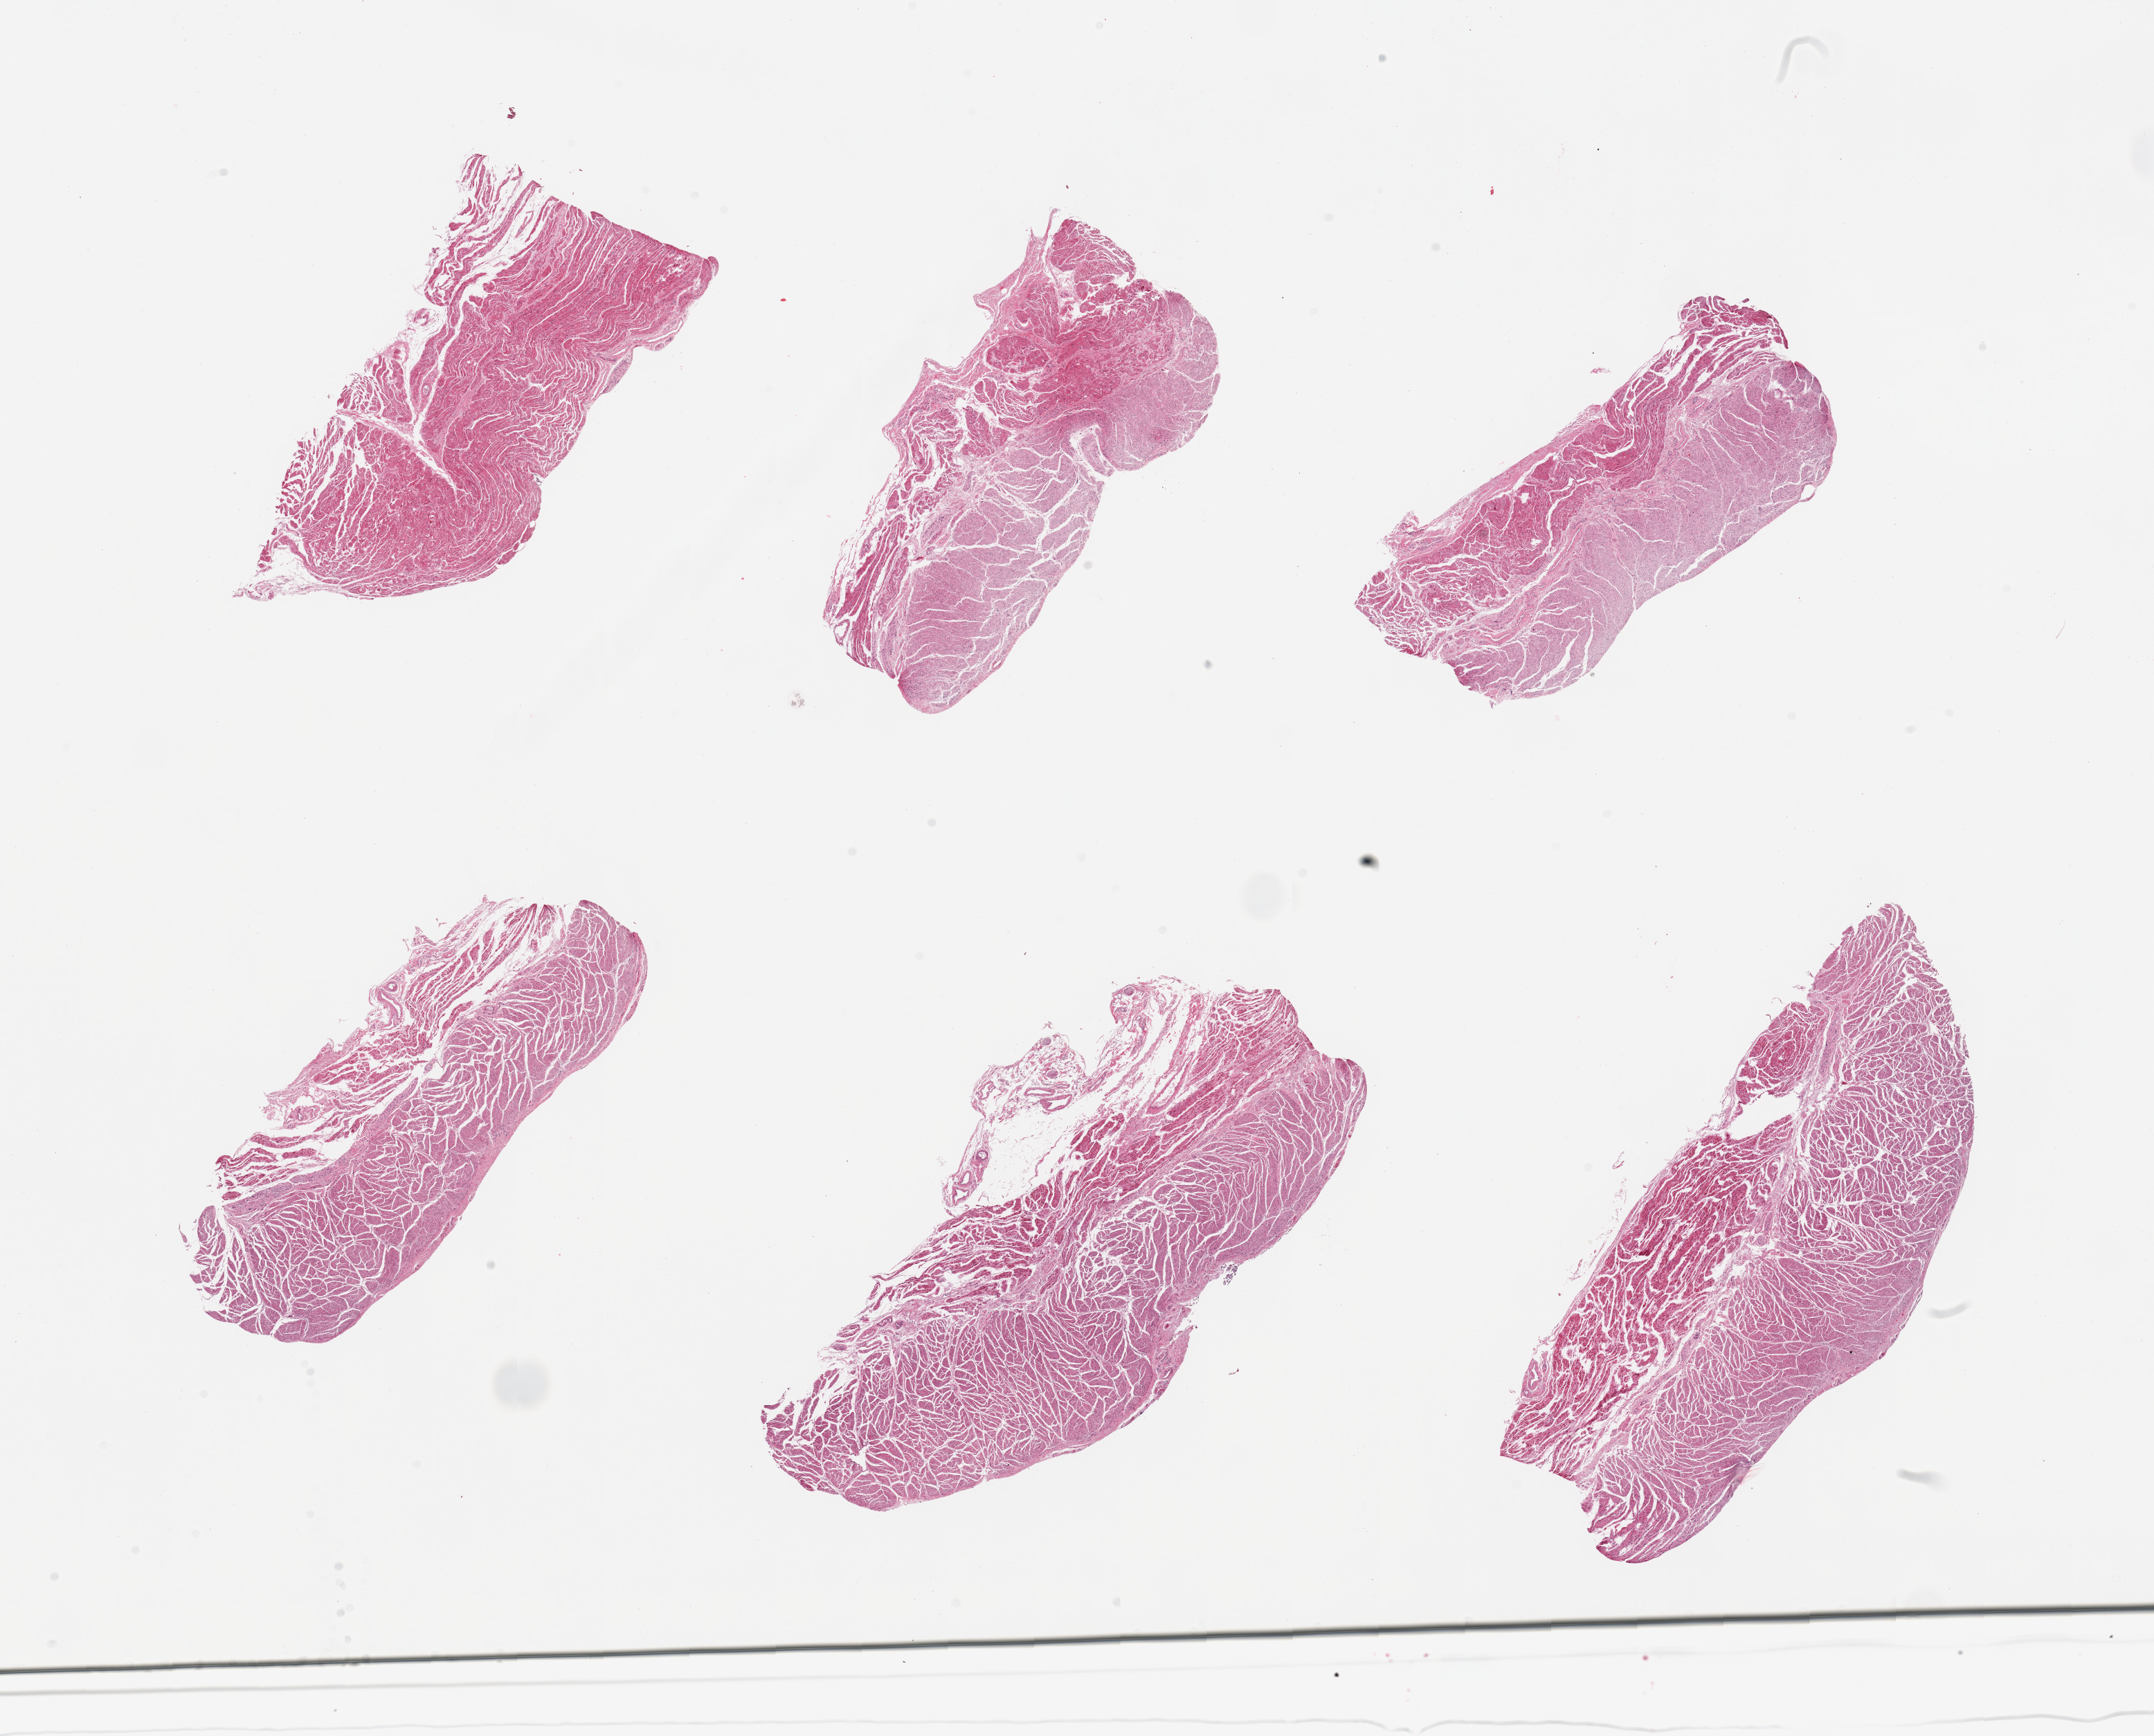
Whole-slide image, haematoxylin and eosin stain, shown as a low-resolution overview of the whole scanned area (about 24.6 x 19.8 mm, from a 20x scan), PAXgene-fixed paraffin-embedded (PFPE) section, sampled site (target tissue): gastroesophageal junction, tissue donor sample.
Review note (as recorded): 6 pieces, target muscularis.